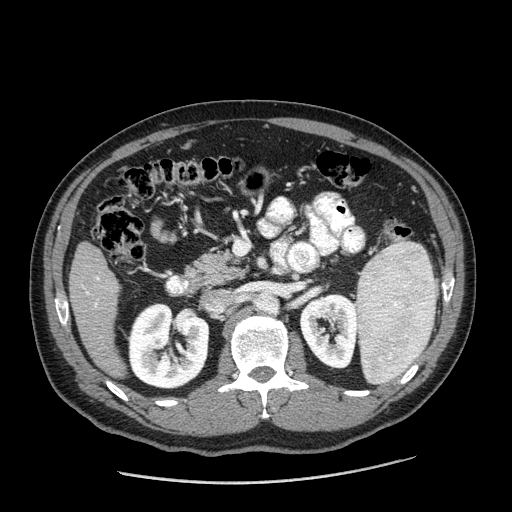
Contrast-enhanced abdominal CT (liver protocol), one axial slice; 120 kVp; one of 2 acquisitions stored at this slice position; soft-tissue window (W 400 / L 40 HU); 2.5 mm slice thickness; 512 × 512 image matrix, field of view 400 × 400 mm. Case-level facts recorded for this patient, not image findings: diagnosis: hepatocellular carcinoma (patient treated with transarterial chemoembolisation; whether this scan precedes or follows treatment is not stated here); TNM stage (as recorded): Stage-II; Child-Pugh class: A.
Structures marked on this image (semi-automatic segmentation, software-assisted and operator-edited):
- liver parenchyma outside the tumour (the mass and vessels are separate outlines, so this box may not span the whole liver): bounding box <68,242,126,376> (left, top, right, bottom; pixels)
- liver vessels: <82,277,99,307>